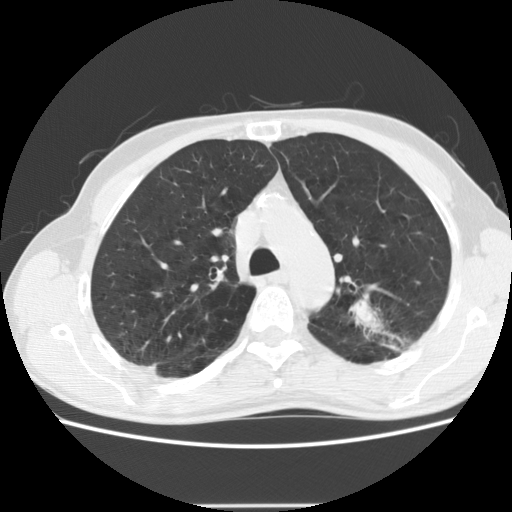
Low-dose screening chest CT, axial slice; first (baseline) screen; lung window (W 1500 / L -600 HU); 2.5 mm slice thickness; standard (soft-tissue) reconstruction kernel (STANDARD); slice 52 of 191 in the series; 512 × 512 image matrix, field of view 352 × 352 mm. Male, age 64 years at enrolment. Current smoker at enrolment.
Expert-annotated lung lesion, bounding box <338,280,441,361> (left, top, right, bottom; pixels). Screening reader's record for this exam (one nodule recorded; not confirmed to be the boxed lesion): non-calcified nodule or mass ≥4 mm, left upper lobe, 27 × 19 mm, poorly defined margins, soft tissue attenuation. Official screen result: positive, change unspecified: nodule(s) >= 4 mm or enlarging nodule(s), mass(es), or other non-specific abnormalities suspicious for lung cancer. Later outcome: lung cancer diagnosed 23 days after this screen — adenocarcinoma, NOS, left upper lobe, moderately differentiated (G2), stage IA (AJCC 6th edition), 29 mm at pathology.